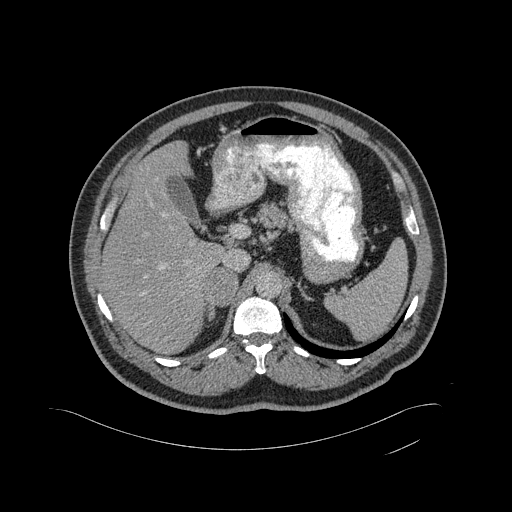
Contrast-enhanced abdominal CT, one axial slice; slice 325 of 433 in the series (ordered by position); 120 kVp; soft-tissue window (W 400 / L 40 HU); 2 mm slice thickness; 512 × 512 image matrix, field of view 500 × 500 mm. Patient: male, 56 years. From the clinical record (not read from this slice): diagnosis: adrenocortical carcinoma; tumour side: right adrenal; tumour size at pathology: 11.6 cm; Ki-67 index: 50 %; stage (as recorded): 3.
Annotated regions visible in this slice (semi-automatic segmentation, software-assisted and operator-edited):
- mass: box from (x=205, y=268) to (x=237, y=304) px